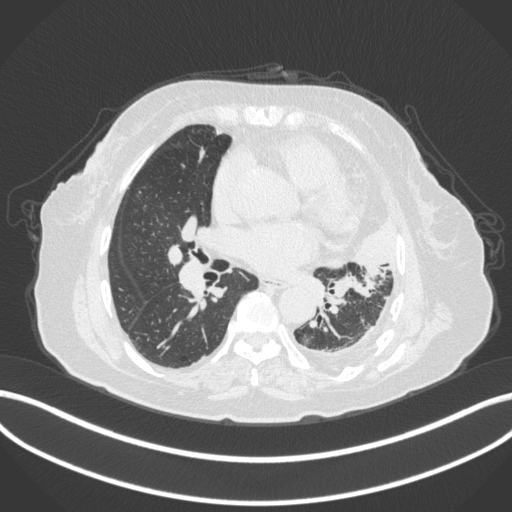
Chest CT, one axial slice; slice 179 of 399 in the series (ordered by position); lung window (W 1500 / L -600 HU); 1 mm slice thickness; 512 × 512 image matrix, field of view 400 × 400 mm. Patient: female, 75 years. Case-level facts recorded for this patient, not image findings: clinical TNM (as recorded): T3 N3 M1.
Outlined on this slice (rectangle marked by the reading radiologist):
- lung tumour (recorded histology: adenocarcinoma): bounding box [x1, y1, x2, y2] px = [317, 223, 397, 278]